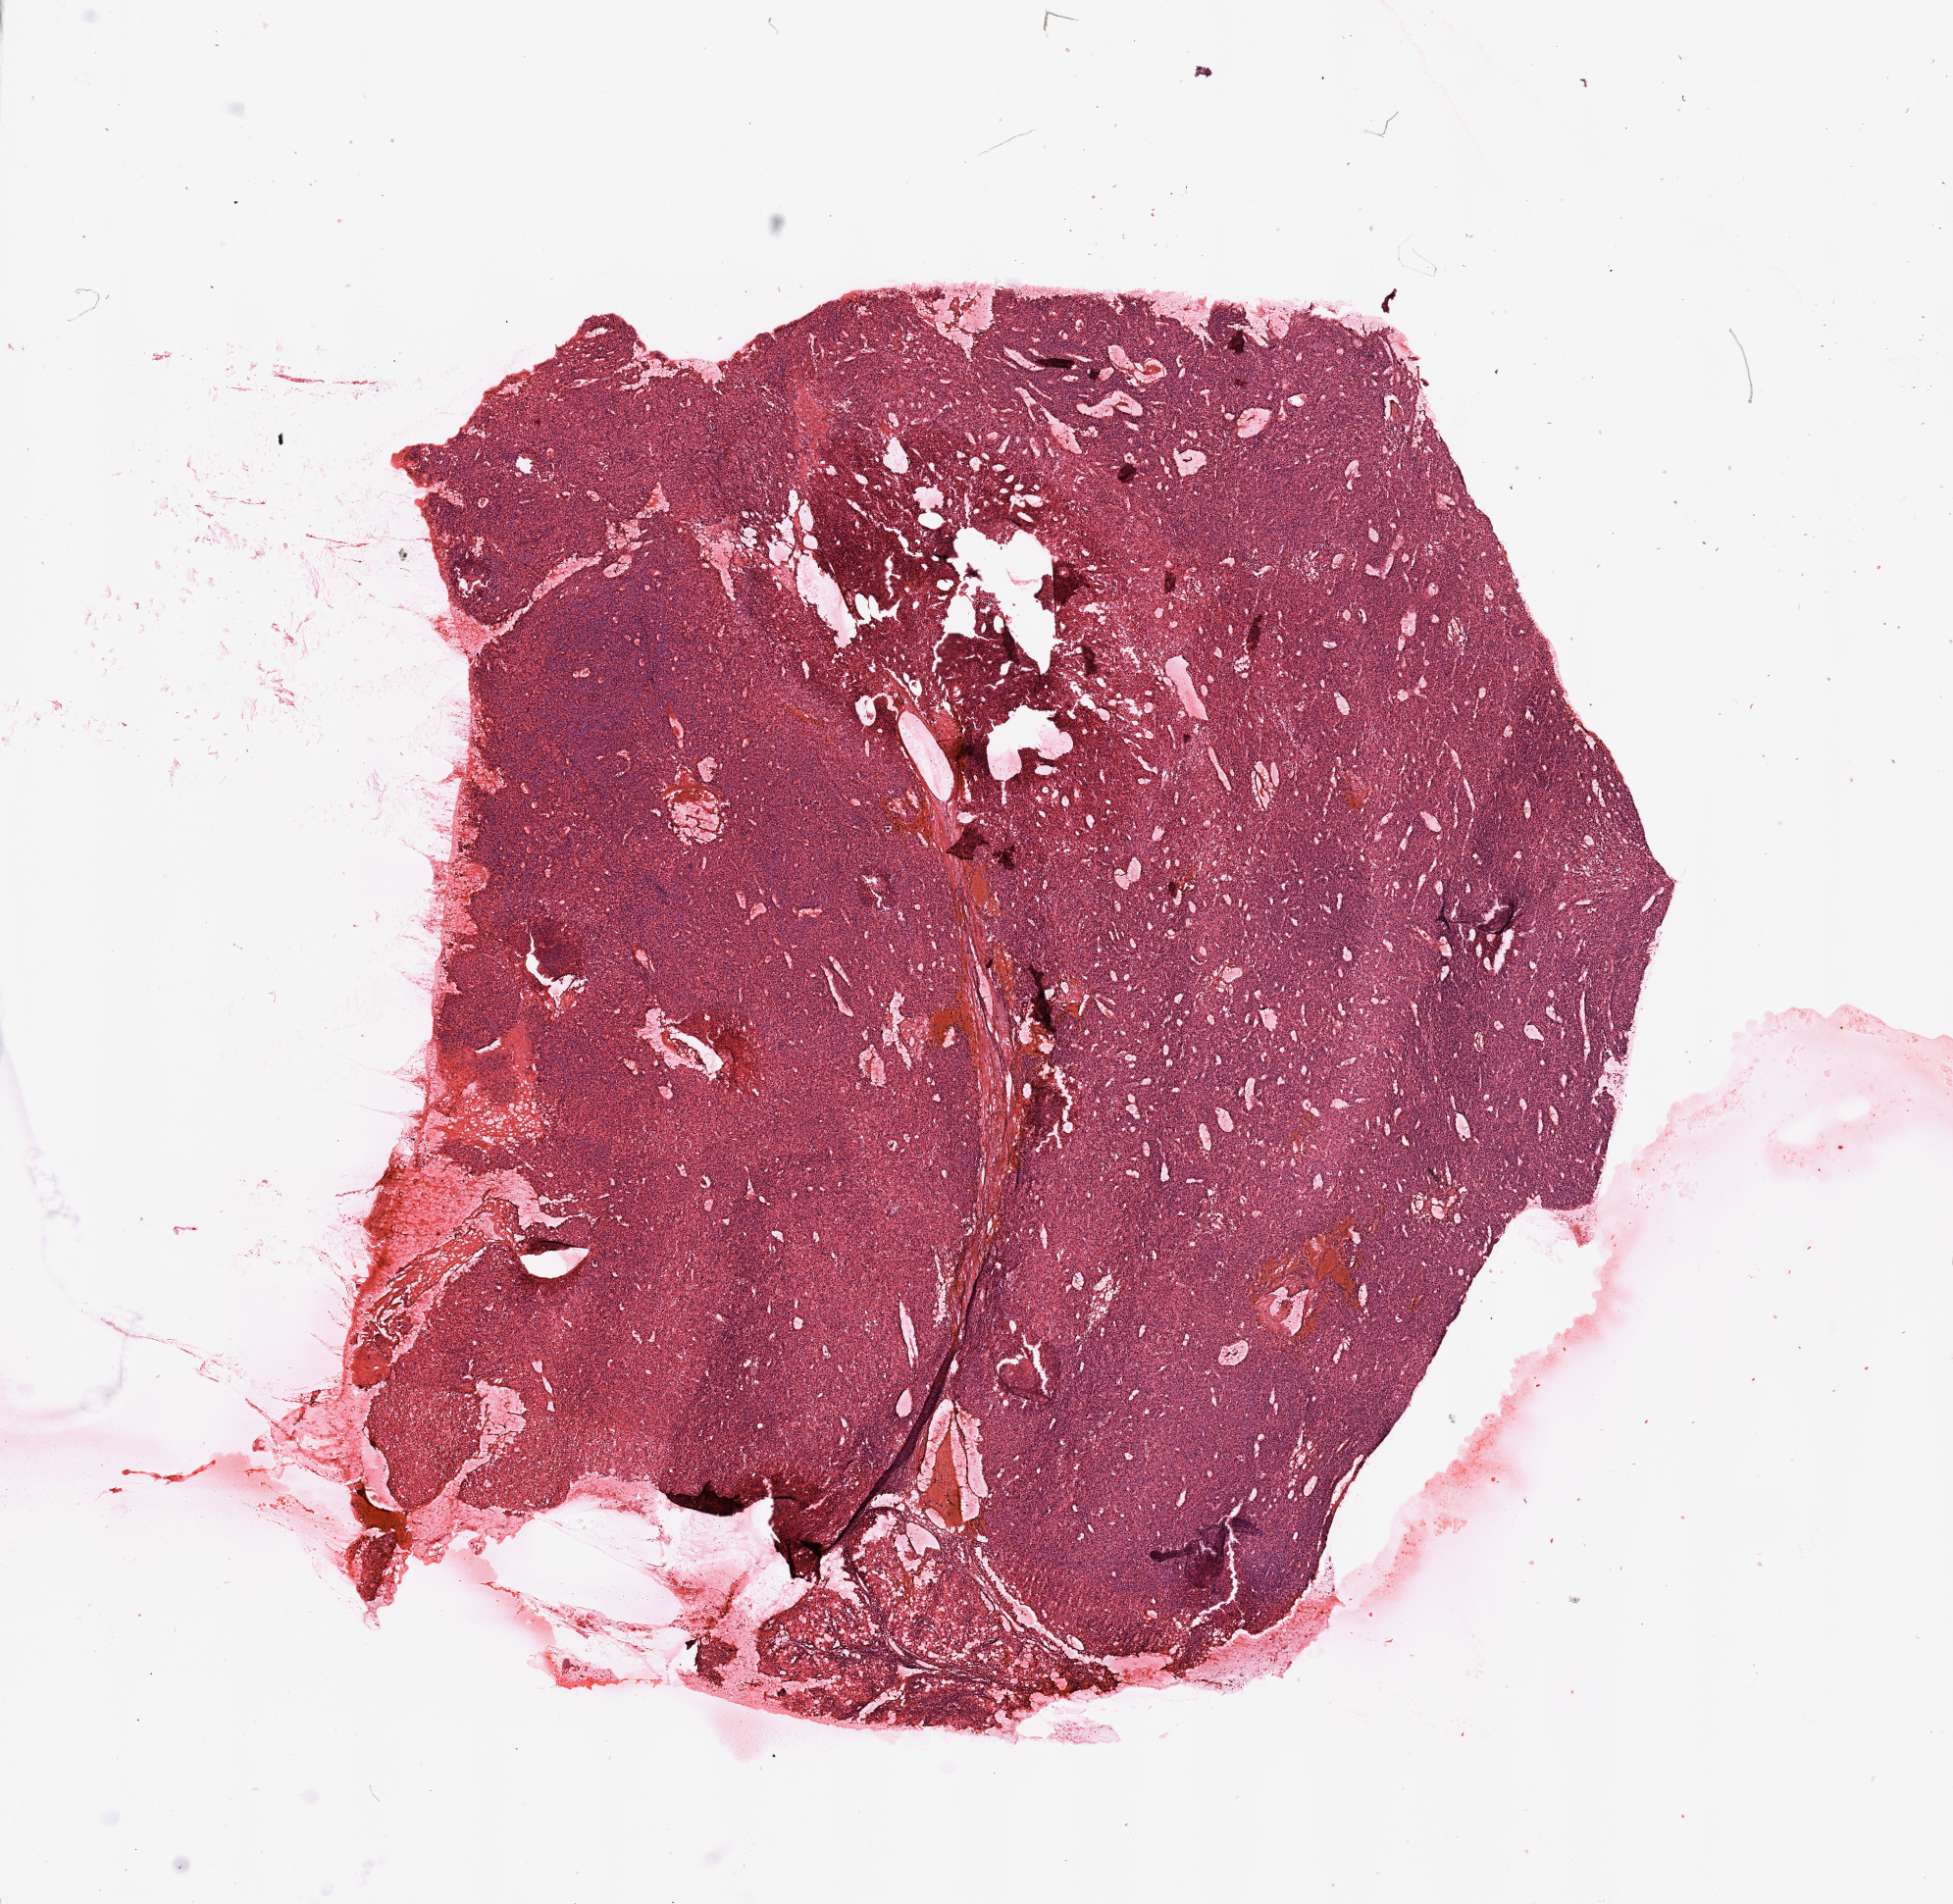
Digitized H&E-stained tissue section (whole slide), whole scanned area (about 15.8 x 15.4 mm, acquisition: 20x scan) shown as a low-resolution overview. Tumour tissue sample, sampled site: kidney. Male, 62 y/o. Histologic grade: G3 (poorly differentiated). Slide review estimates, as recorded: tumour nuclei 90%, necrosis 5%.
- diagnosis: Renal cell carcinoma, NOS
- AJCC pathologic stage: III